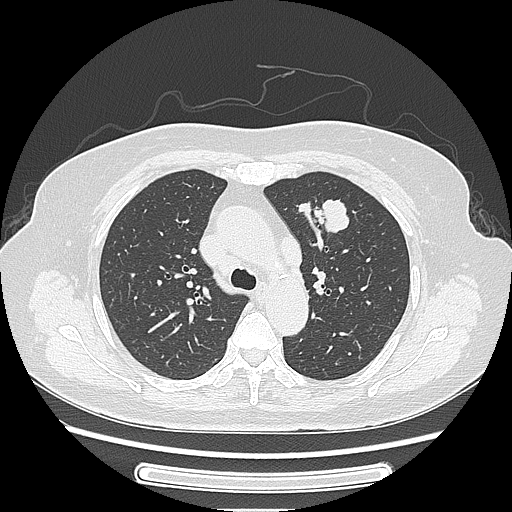
Chest CT, one axial slice. Slice 168 of 227 in the series (ordered by position). Reconstruction kernel LUNG. 120 kVp. Lung window (W 1500 / L -600 HU). 1.25 mm slice thickness. 512 × 512 image matrix. Female patient, age 77 years. From the clinical record (not read from this slice): clinical TNM (as recorded): T1c N3 M0; histopathological grade: G2-3.
Structures marked on this image (bounding box drawn by a radiologist):
- lung tumour (recorded histology: adenocarcinoma): bounding box (x1, y1, x2, y2) in pixels: (313, 193, 352, 241)